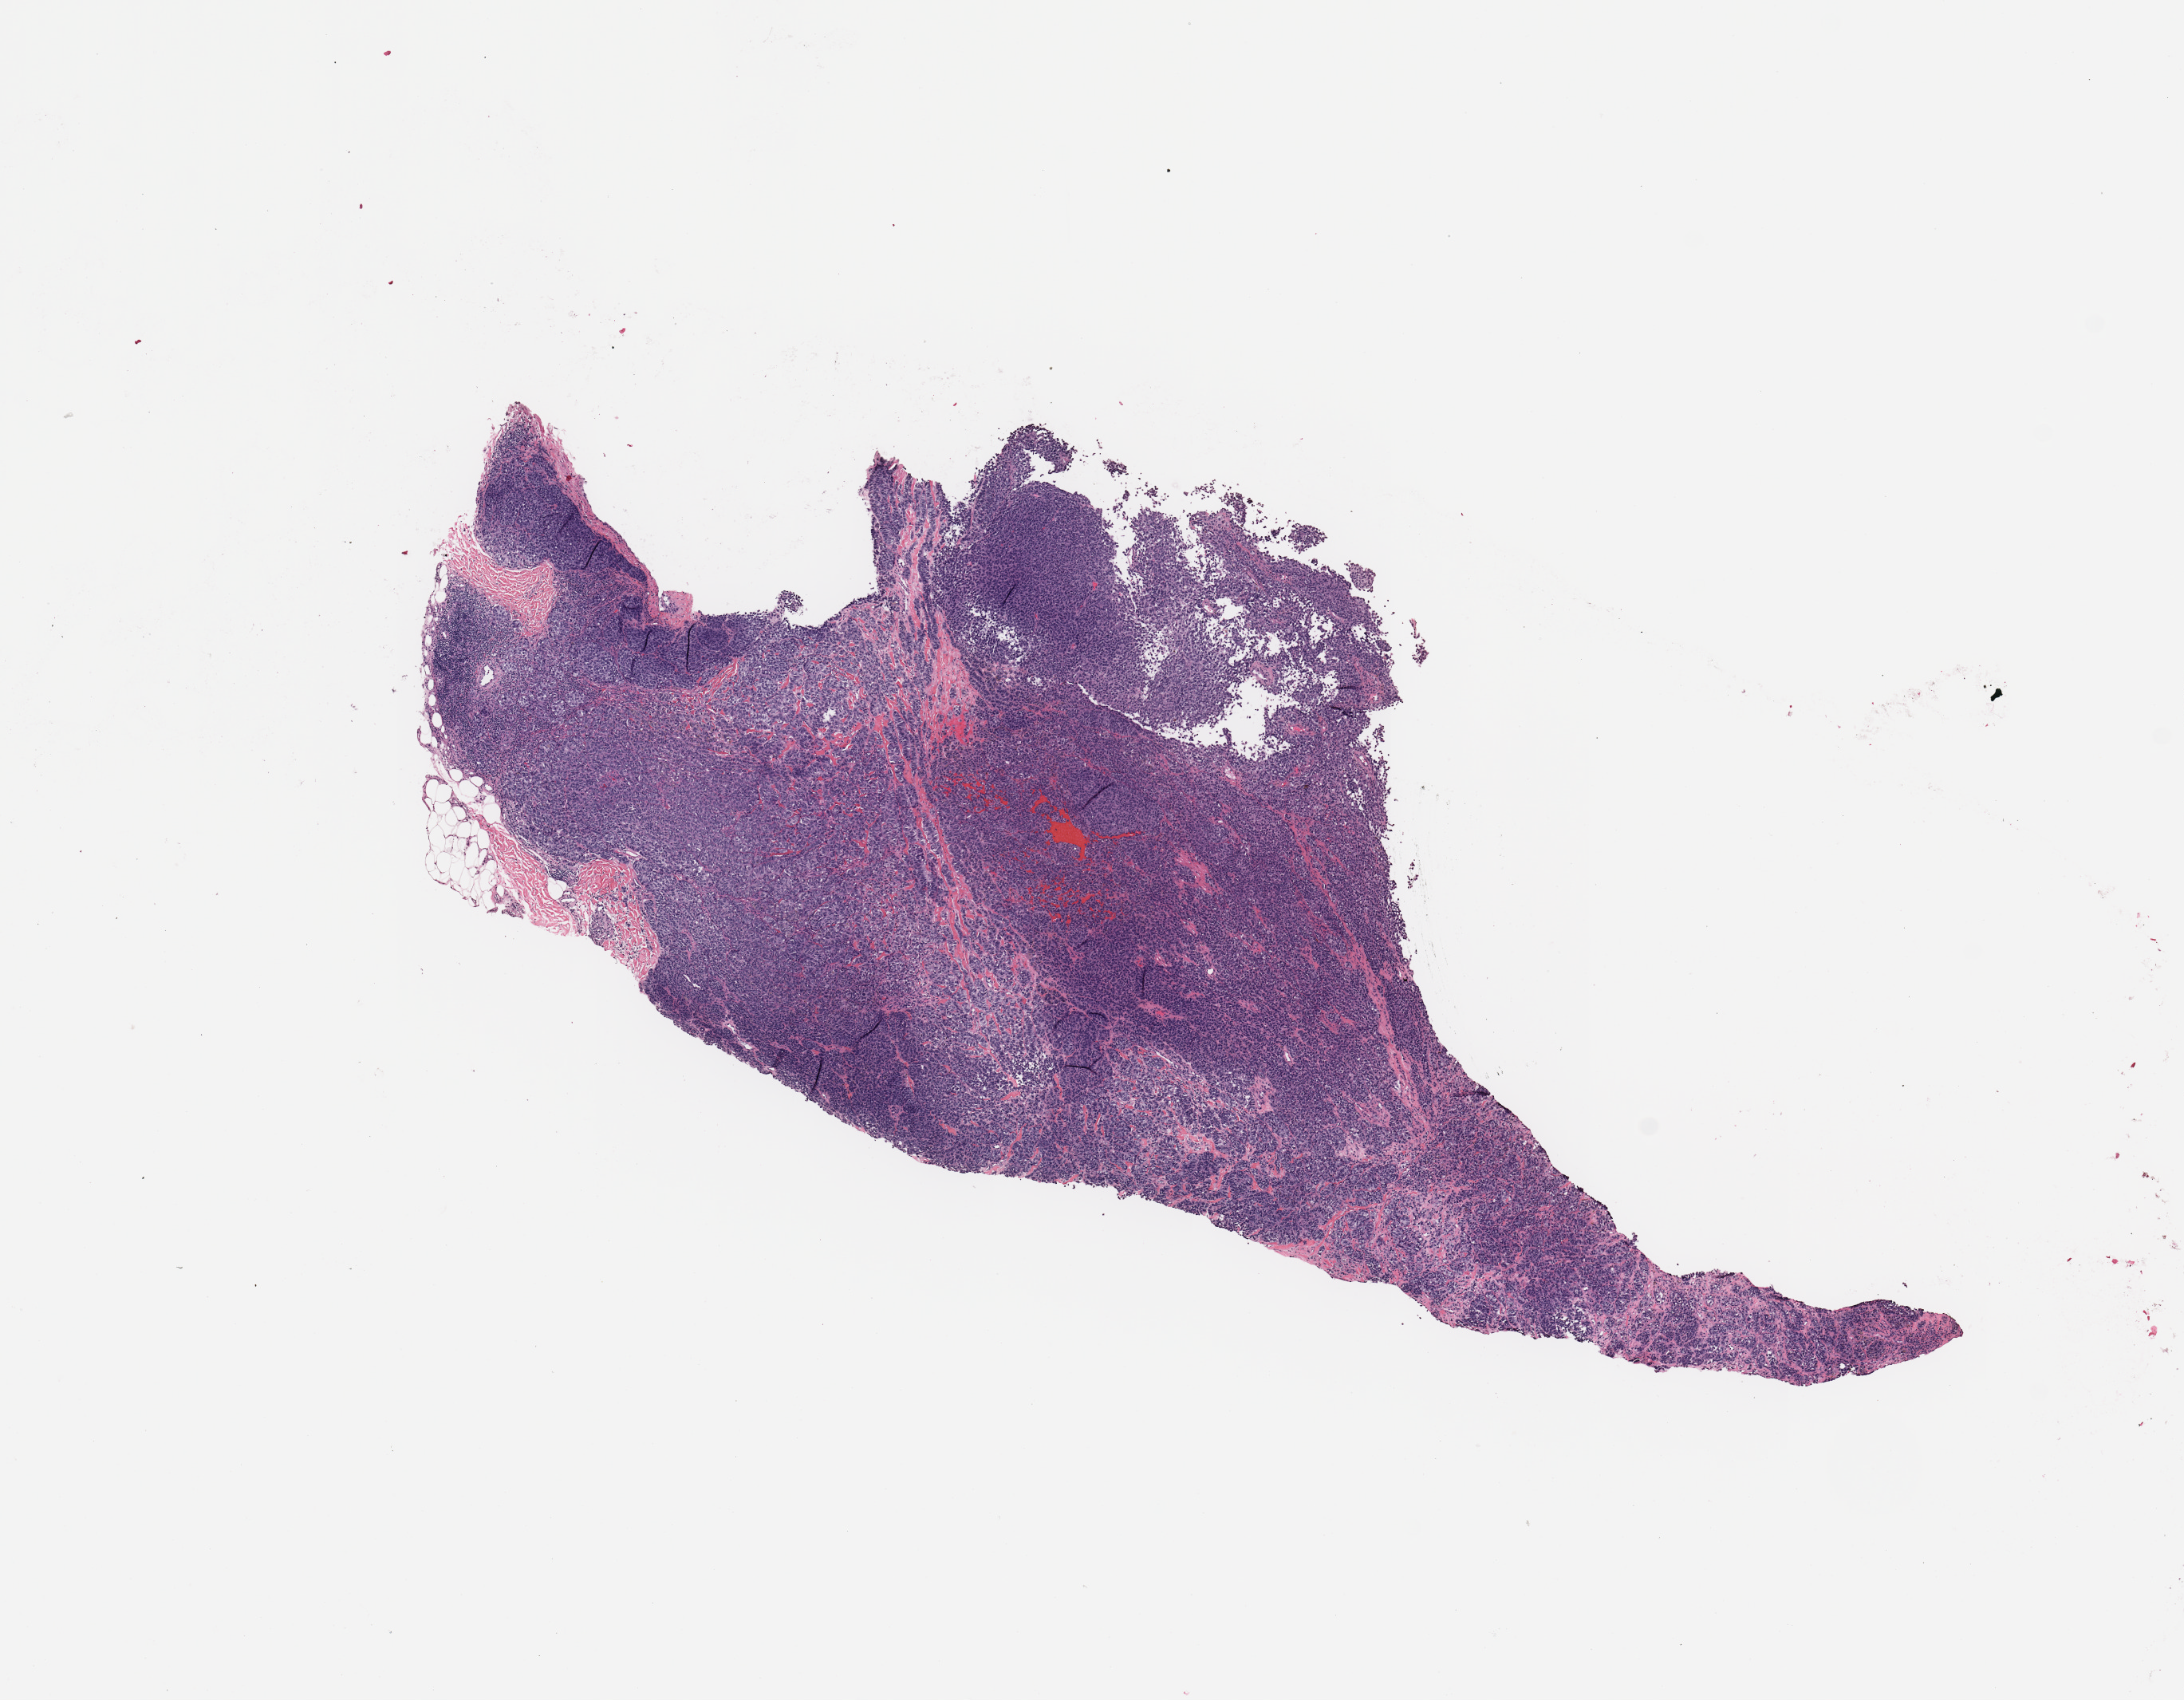
Whole-slide histology image, H&E-stained, shown as a low-resolution overview of the whole scanned area (about 10.8 x 8.4 mm). Melanoma tumour tissue; sampled site not recorded. 73-year-old female patient.
* diagnosis: Malignant melanoma, NOS
* AJCC pathologic stage: IIB
* primary tumour site (as recorded): extremities